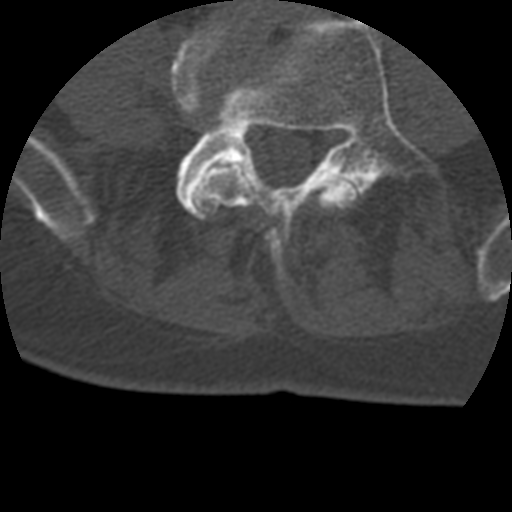
CT including the spine, one axial slice. Slice 51 of 399 in the series (ordered by position). Reconstruction kernel STANDARD. 120 kVp. Bone window (W 1800 / L 400 HU). 1.25 mm slice thickness. 512 × 512 image matrix, field of view 160 × 160 mm. Patient age 69 years. Case-level facts recorded for this patient, not image findings: primary cancer: prostate.
Outlined on this slice (semi-automatic segmentation, software-assisted and operator-edited):
- L4 vertebra: bounding box <171,20,360,279> (left, top, right, bottom; pixels)
- L5 vertebra: <176,17,432,218>